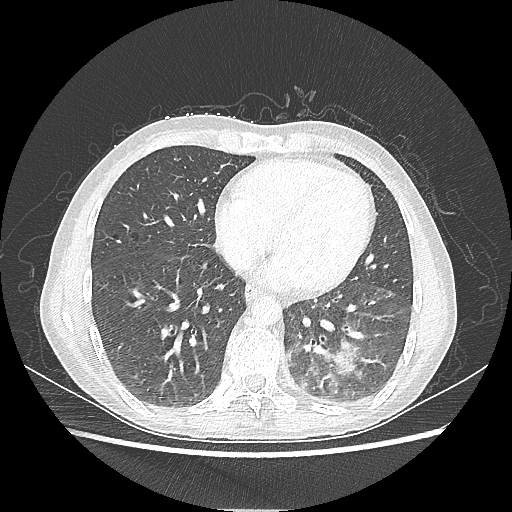
Chest CT, one axial slice. Slice 82 of 220 in the series (ordered by position). Reconstruction kernel LUNG. 80 kVp. Lung window (W 1500 / L -600 HU). 1.25 mm slice thickness. 512 × 512 image matrix, field of view 360 × 360 mm. Female patient, age 53 years. From the clinical record (not read from this slice): clinical TNM (as recorded): T3 N0 M0.
Outlined on this slice (rectangle marked by the reading radiologist):
- lung tumour (recorded histology: adenocarcinoma): bounding box (x1, y1, x2, y2) in pixels: (308, 335, 361, 379)